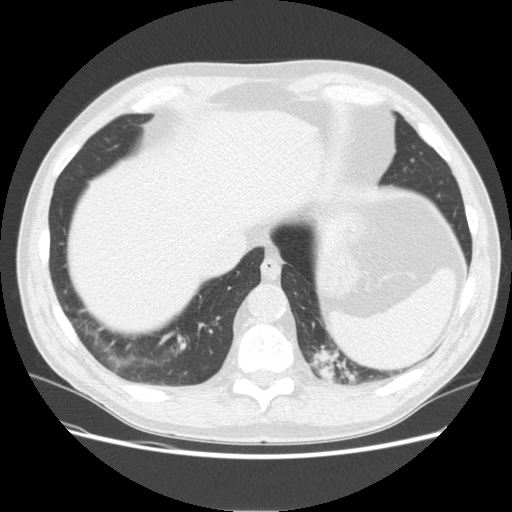
Low-dose screening chest CT, one axial slice; slice 46 of 165 in the series (ordered by position); reconstruction kernel STANDARD; lung window (W 1500 / L -600 HU); 2.5 mm slice thickness; 512 × 512 image matrix, field of view 375 × 375 mm.
Structures marked on this image (manually delineated by an expert):
- lesion 1 (tumor, upper lobe of left lung): bounding box (x1, y1, x2, y2) in pixels: (310, 347, 358, 383)